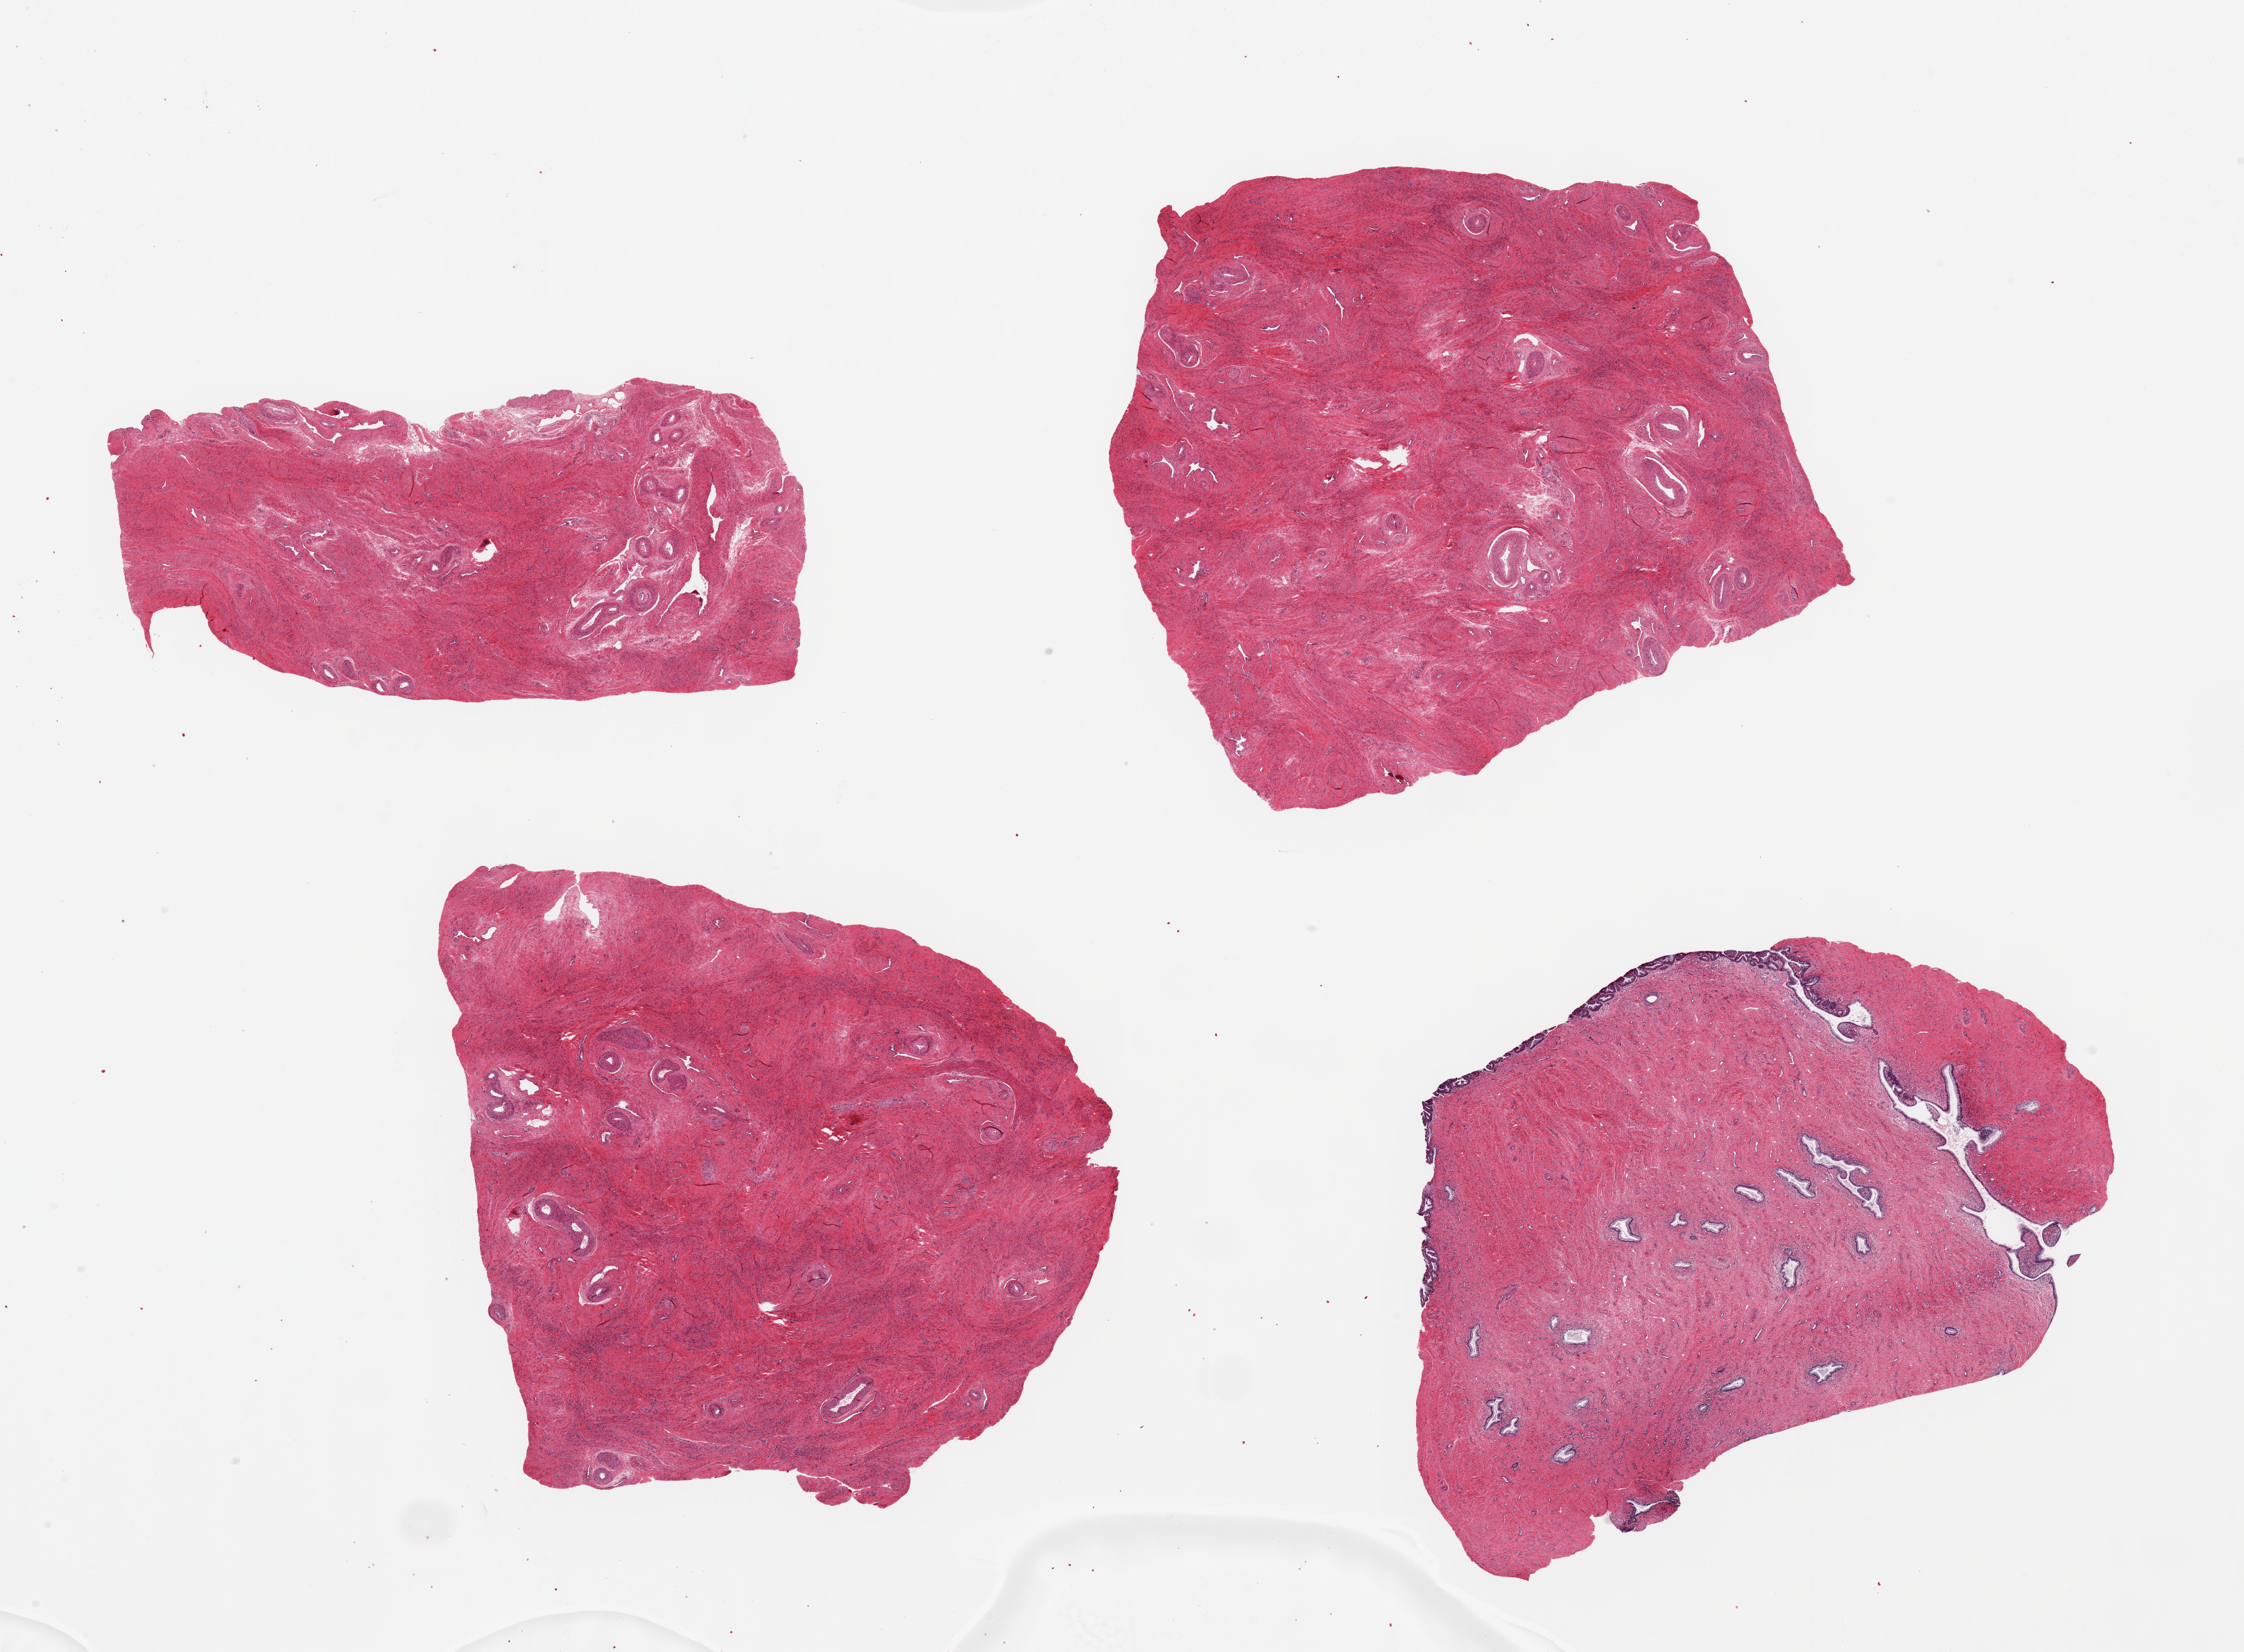
Whole-slide image, H&E stain, low-resolution overview of the scanned area, about 25.6 x 18.8 mm; PAXgene-fixed paraffin-embedded (PFPE) section; sampled site (target tissue): endocervix; tissue donor sample. Donor: female.
Review note (as recorded): 4 aliquots, ~ 7x7mm; One shows endocervical surface mucosa with early squamous metaplasia, and deeper endocervical glands en; other 3 with no glands, only stroma.